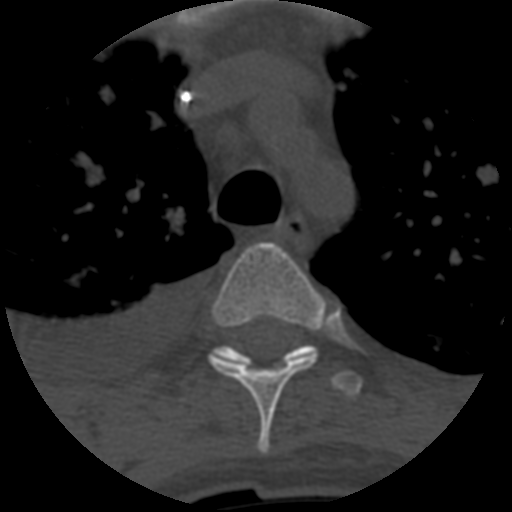
CT including the spine, one axial slice. Slice 466 of 708 in the series (ordered by position). Reconstruction kernel STANDARD. One of 3 acquisitions stored at this slice position. Bone window (W 1800 / L 400 HU). 512 × 512 image matrix, field of view 160 × 160 mm. Patient age 55 years. From the clinical record (not read from this slice): primary cancer: colon.
Annotated regions visible in this slice (semi-automatic segmentation, software-assisted and operator-edited):
- T4 vertebra: bounding box [x1, y1, x2, y2] px = [209, 243, 329, 454]
- T5 vertebra: [212, 344, 363, 397]